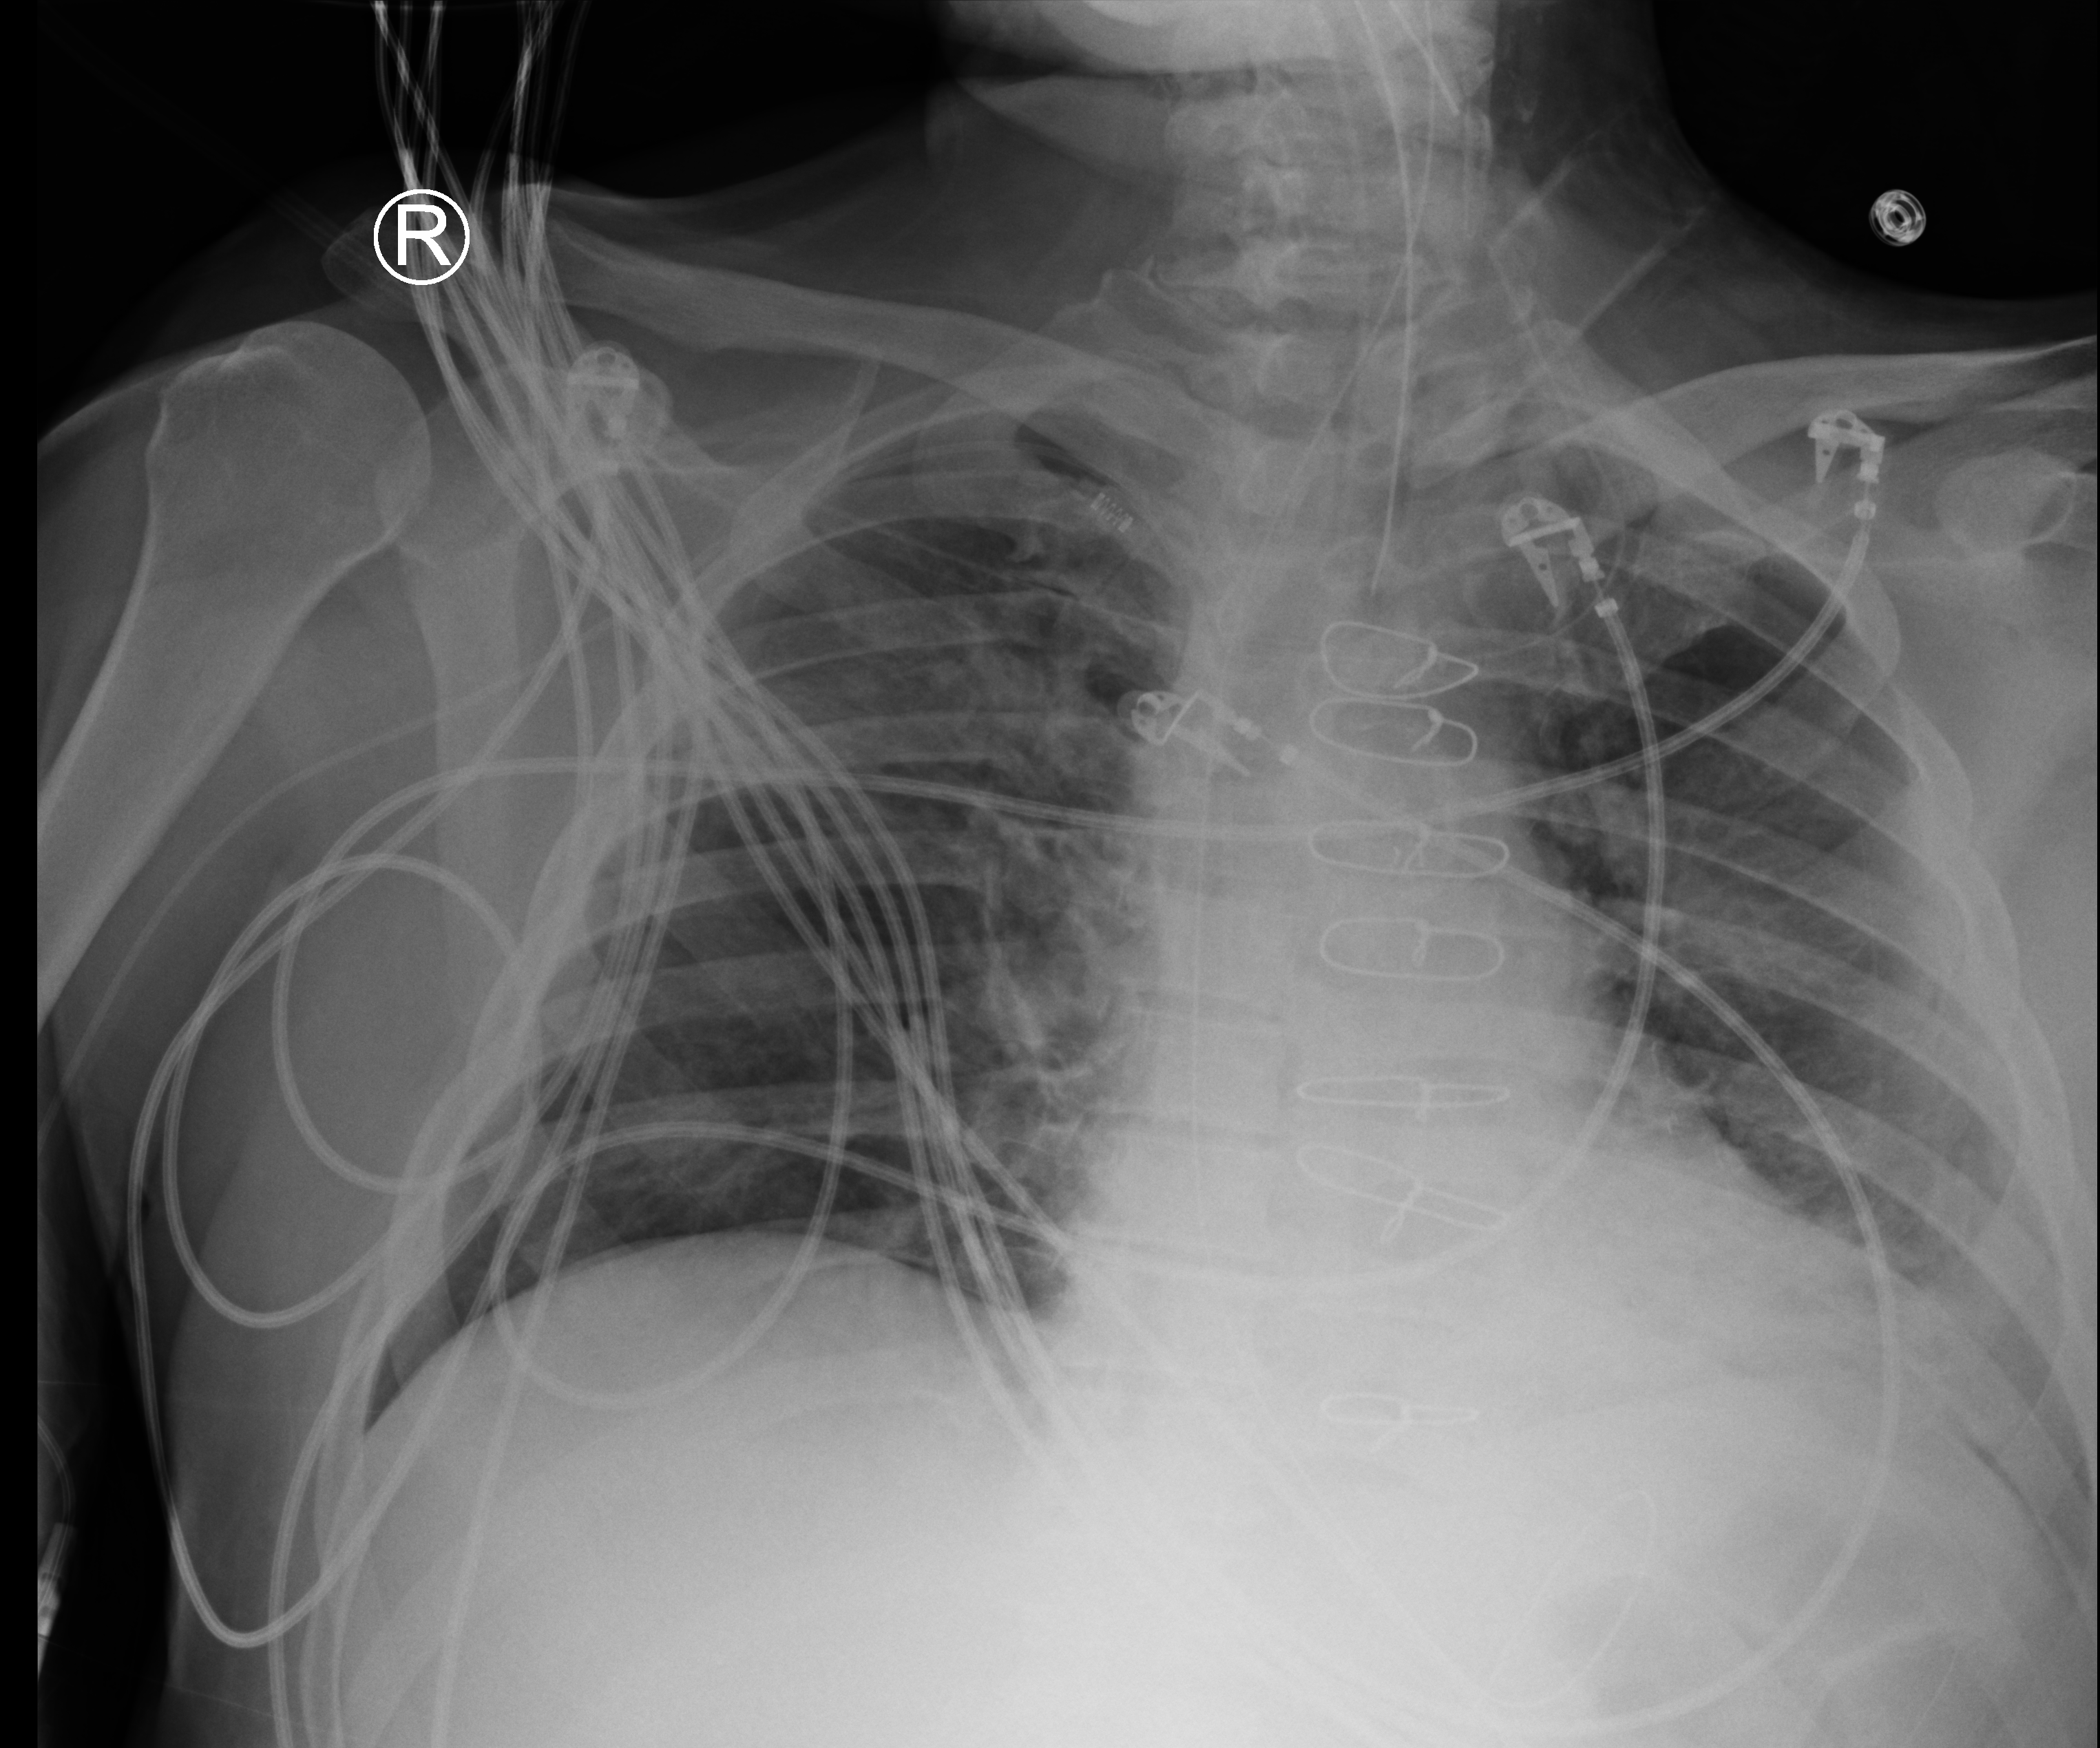
Portable chest radiograph; anteroposterior (AP) projection. Male patient hospitalised with COVID-19, age 60–74 years.
From the hospital-stay record, not from the radiograph (when in the stay this image was taken is not recorded): length of hospital stay: 44 days; mechanically ventilated during this hospital stay: yes.